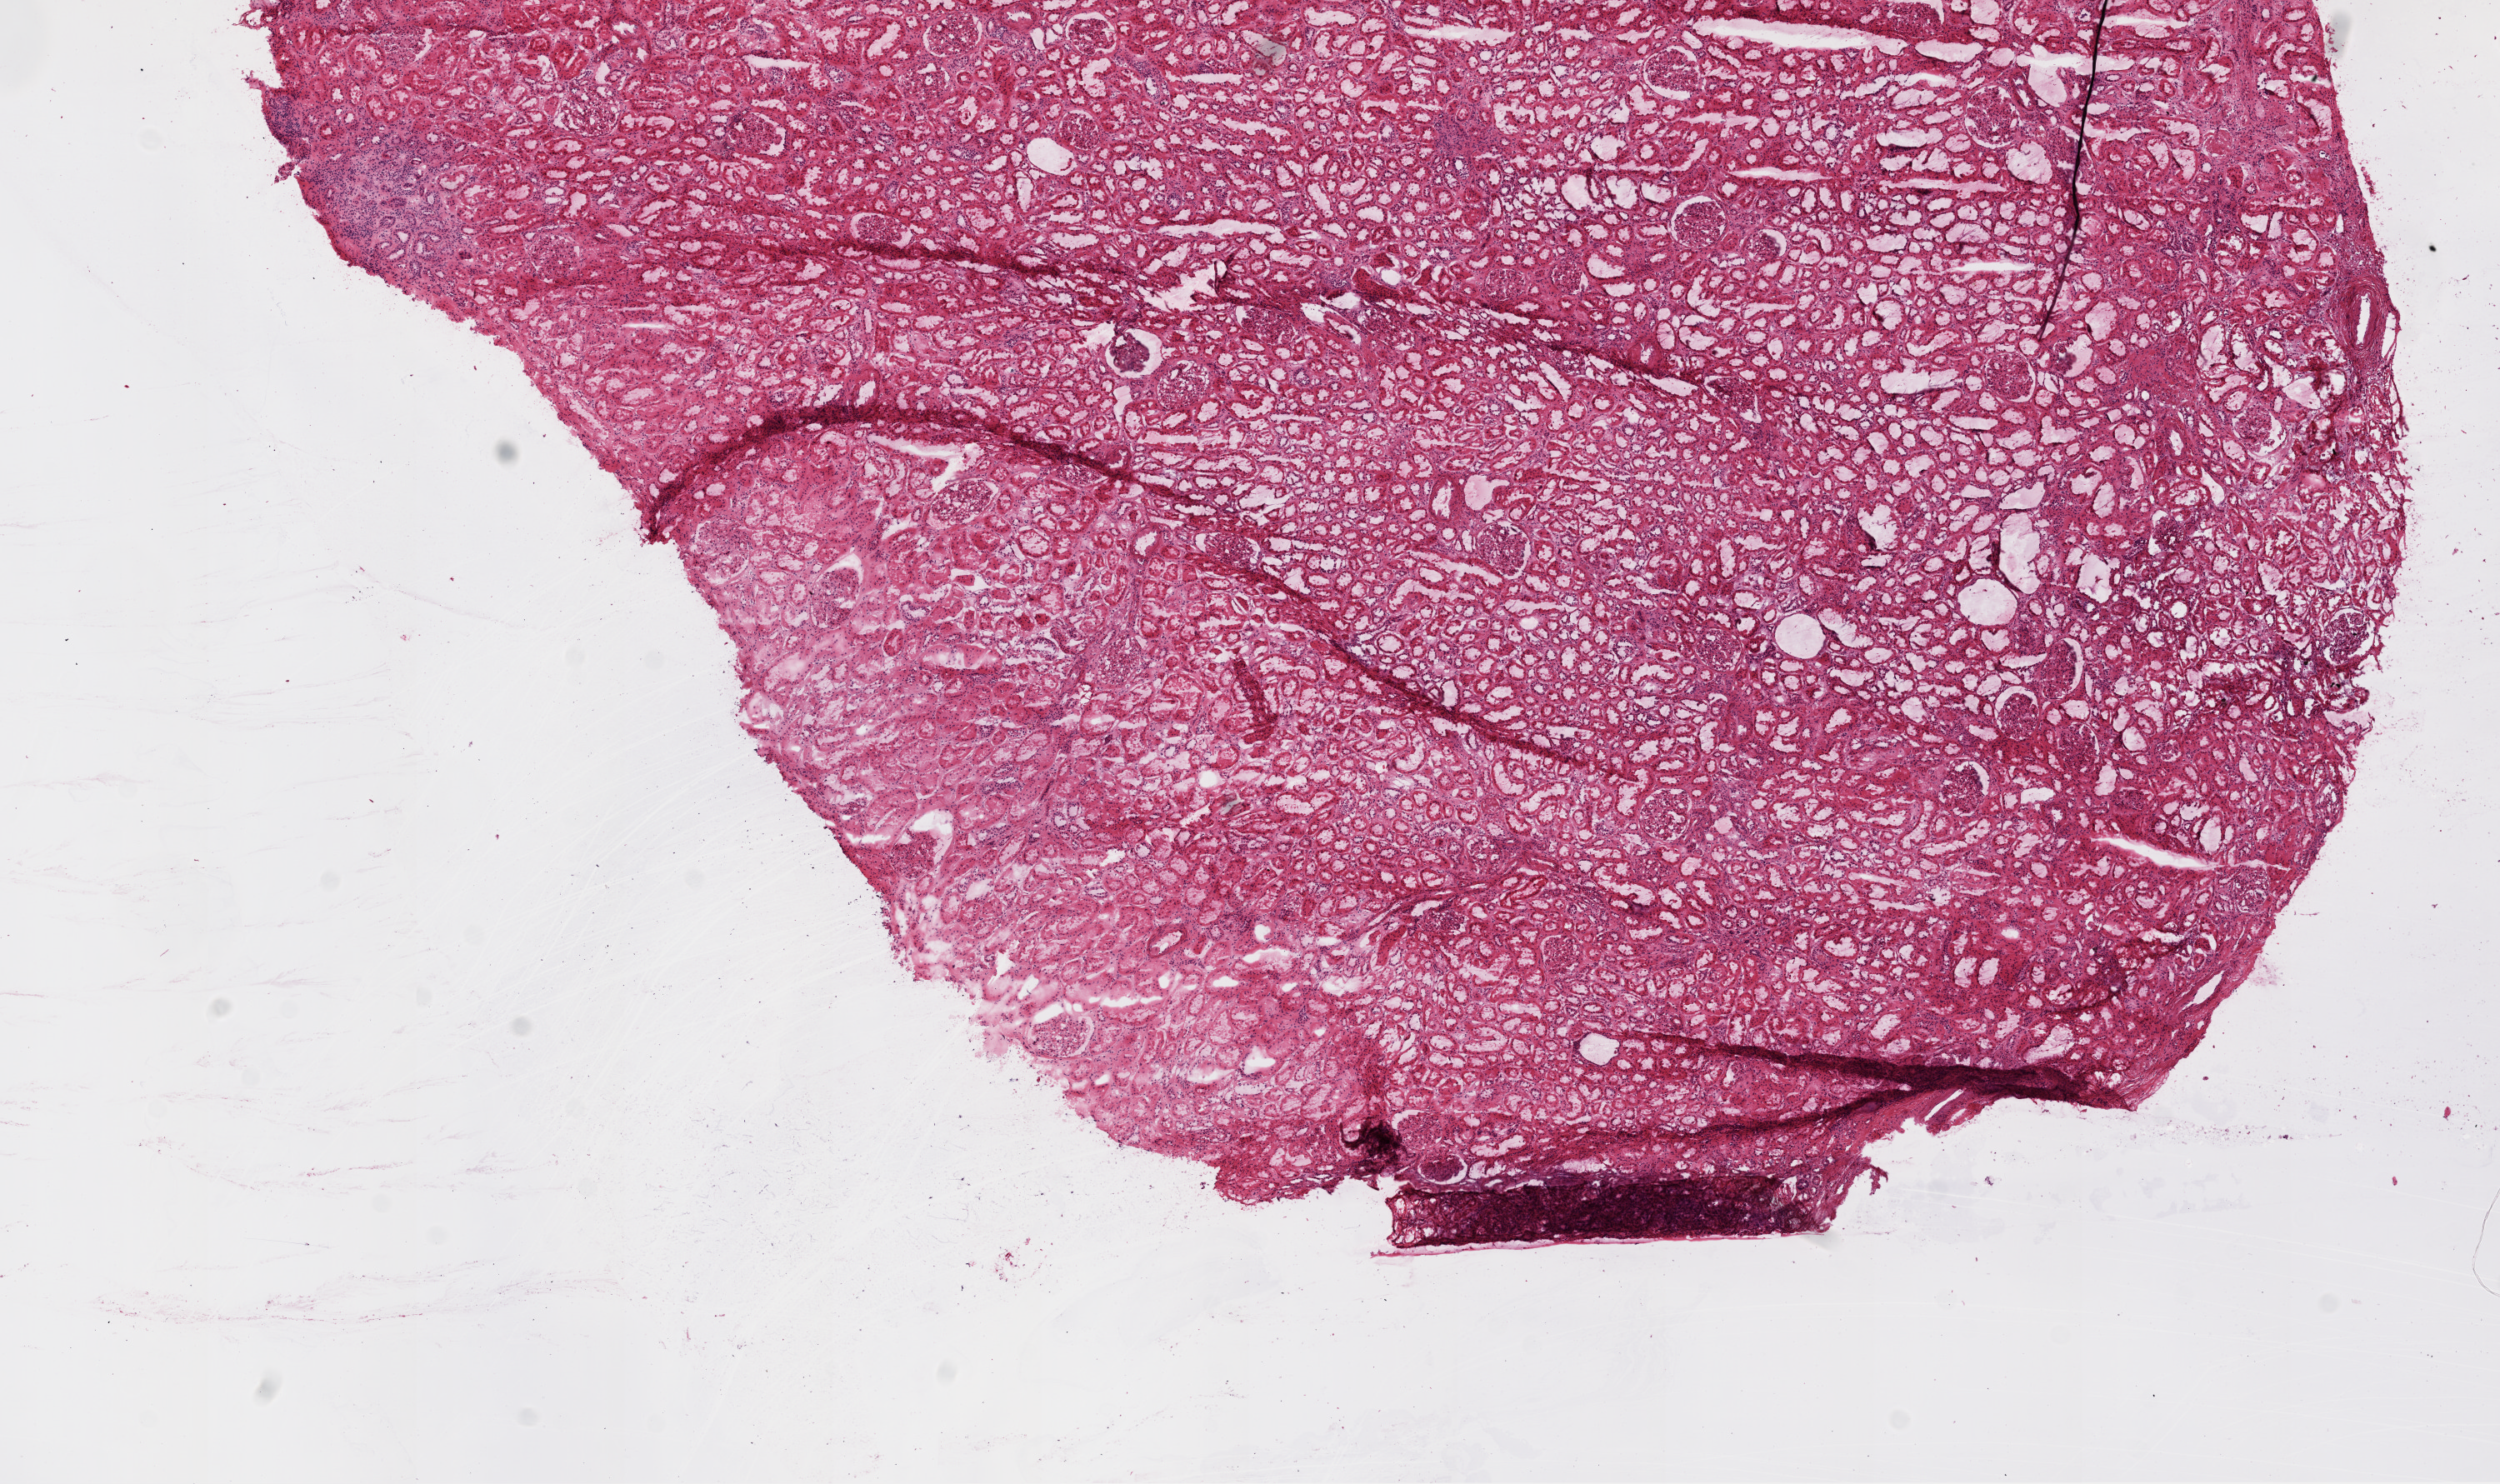
Digitized Hematoxylin and eosin (H&E) stained tissue section (whole slide) — whole scanned area (about 12.0 x 7.1 mm) shown as a low-resolution overview; frozen section; sample: solid tissue normal (non-tumour tissue), kidney. Female patient; age at initial diagnosis 62 years.
• this section: solid tissue normal (non-tumour) sample from the same patient
• patient diagnosis: Clear cell adenocarcinoma, NOS